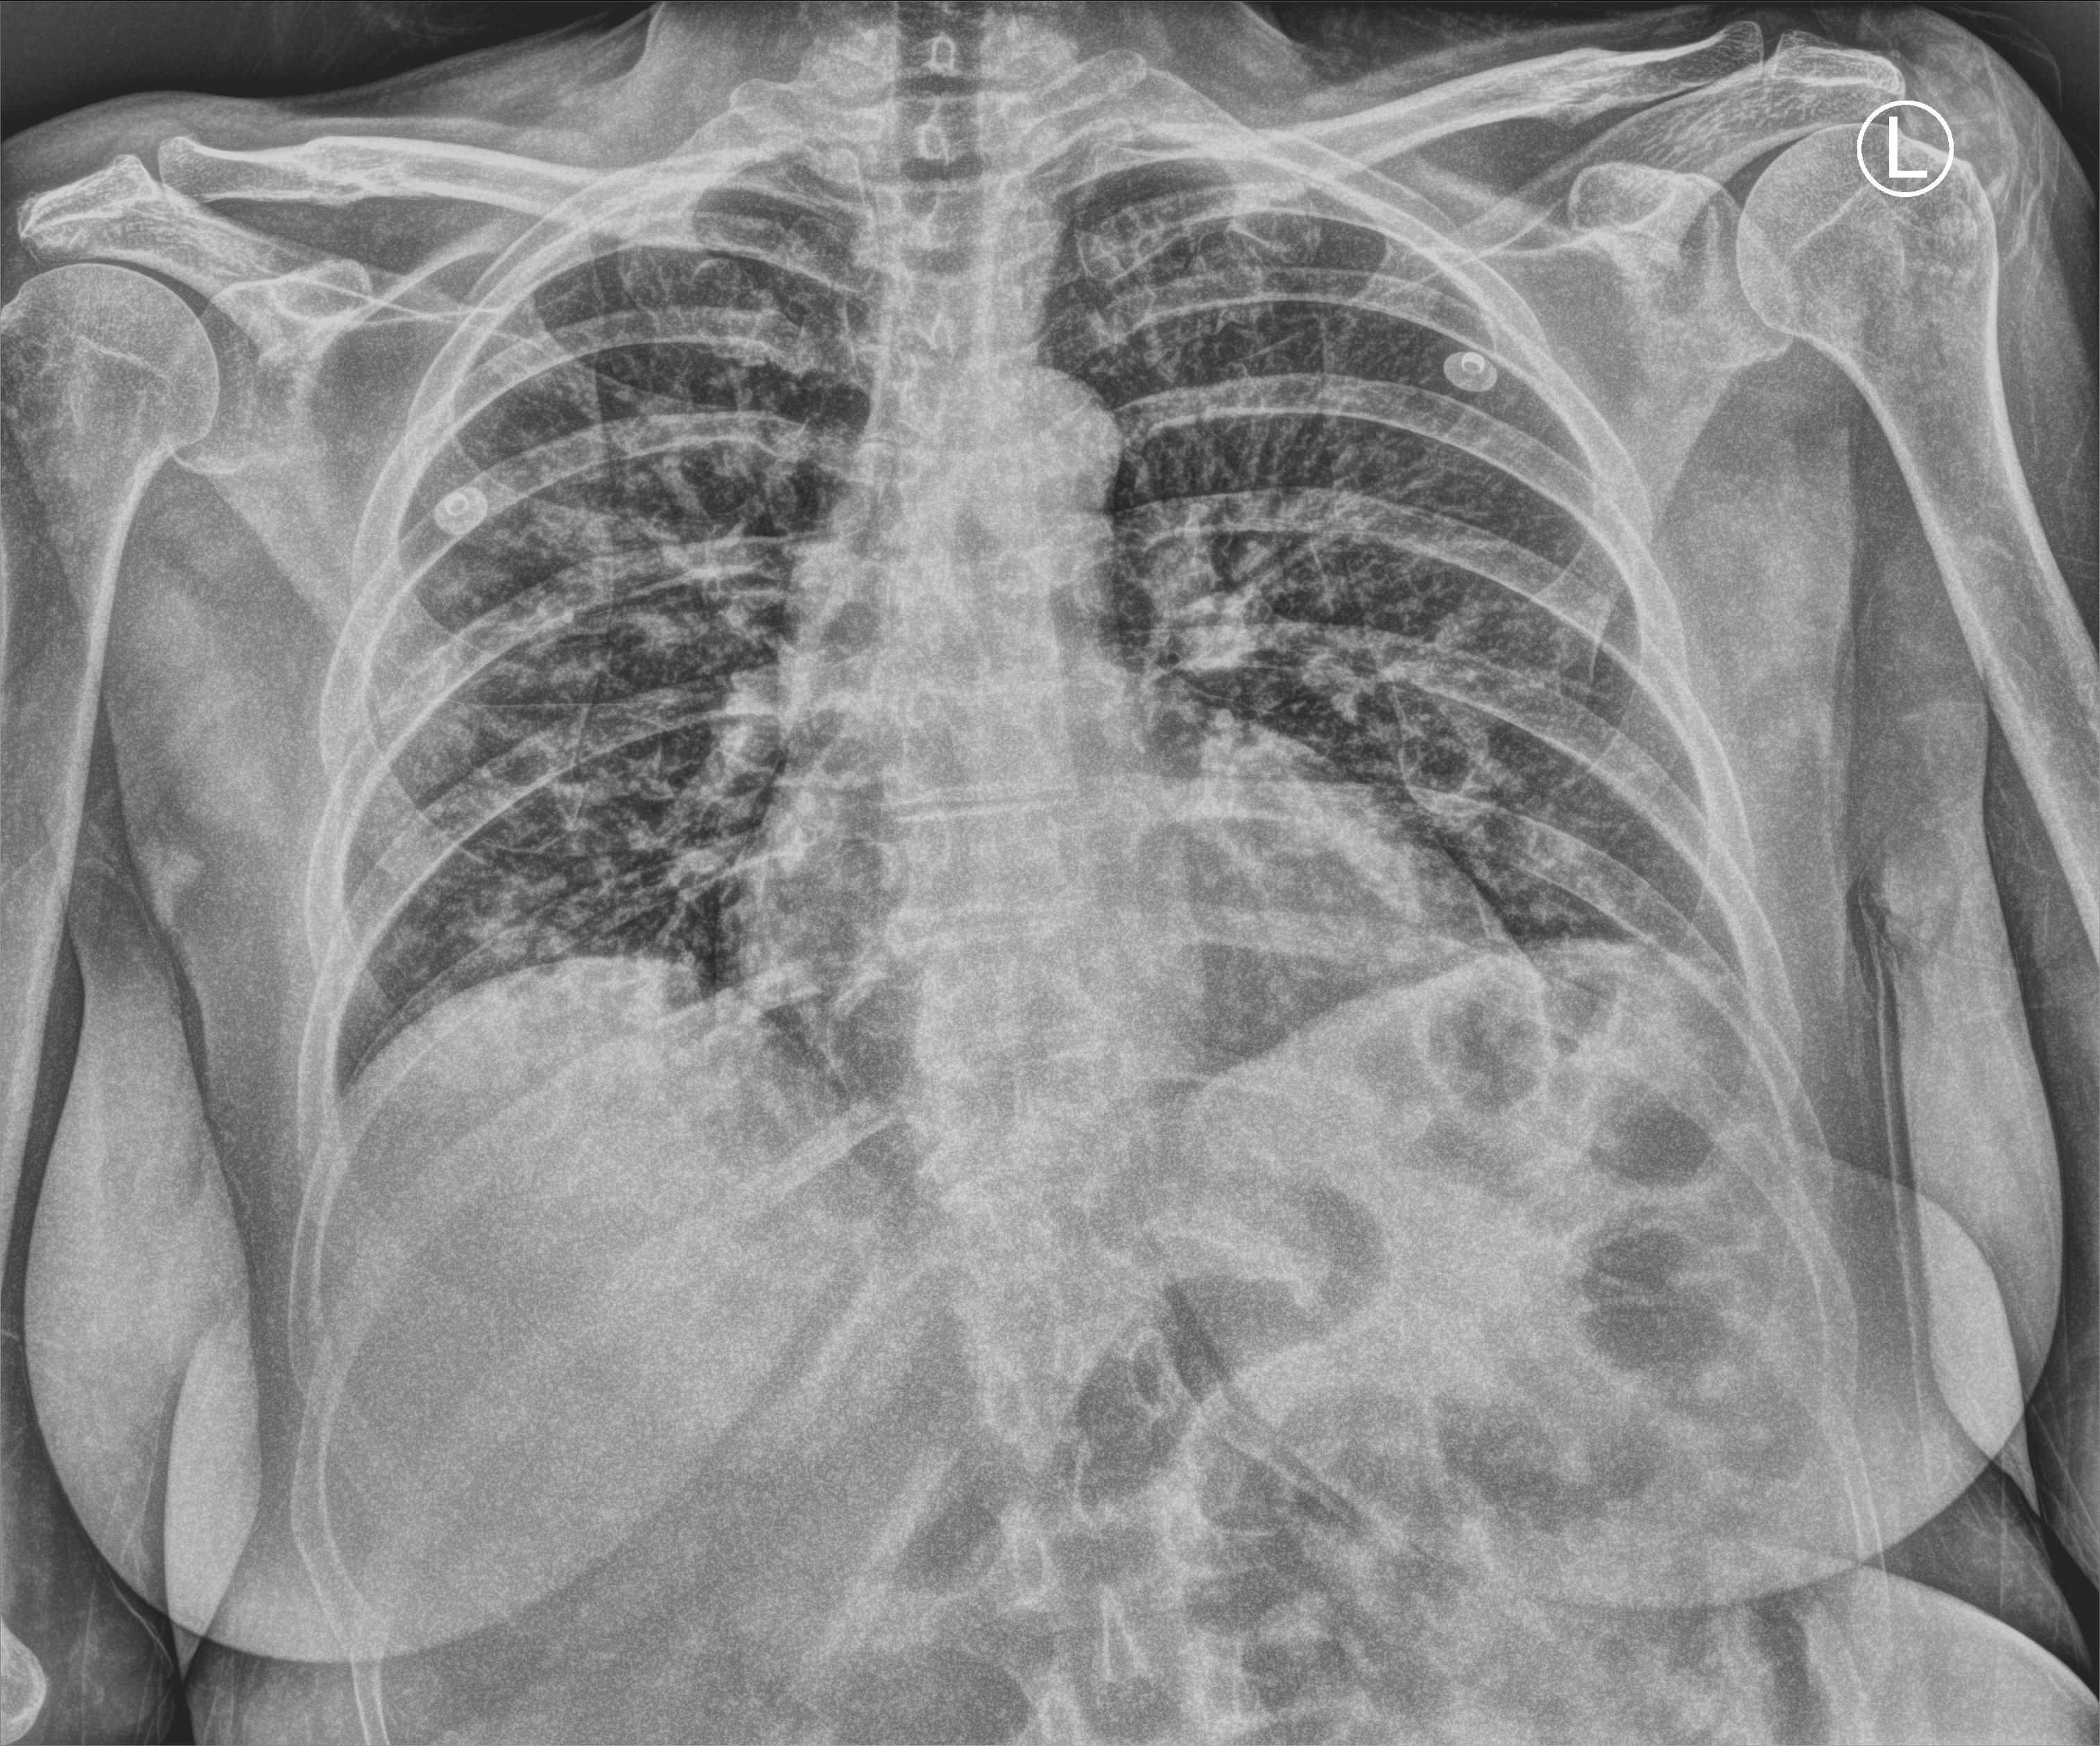
Portable chest radiograph; anteroposterior (AP) projection. Patient hospitalised with COVID-19; female, aged 18–59 years.
Hospital-stay facts (about this admission, not read from this image; timing relative to this image not recorded): length of hospital stay: 3 days.